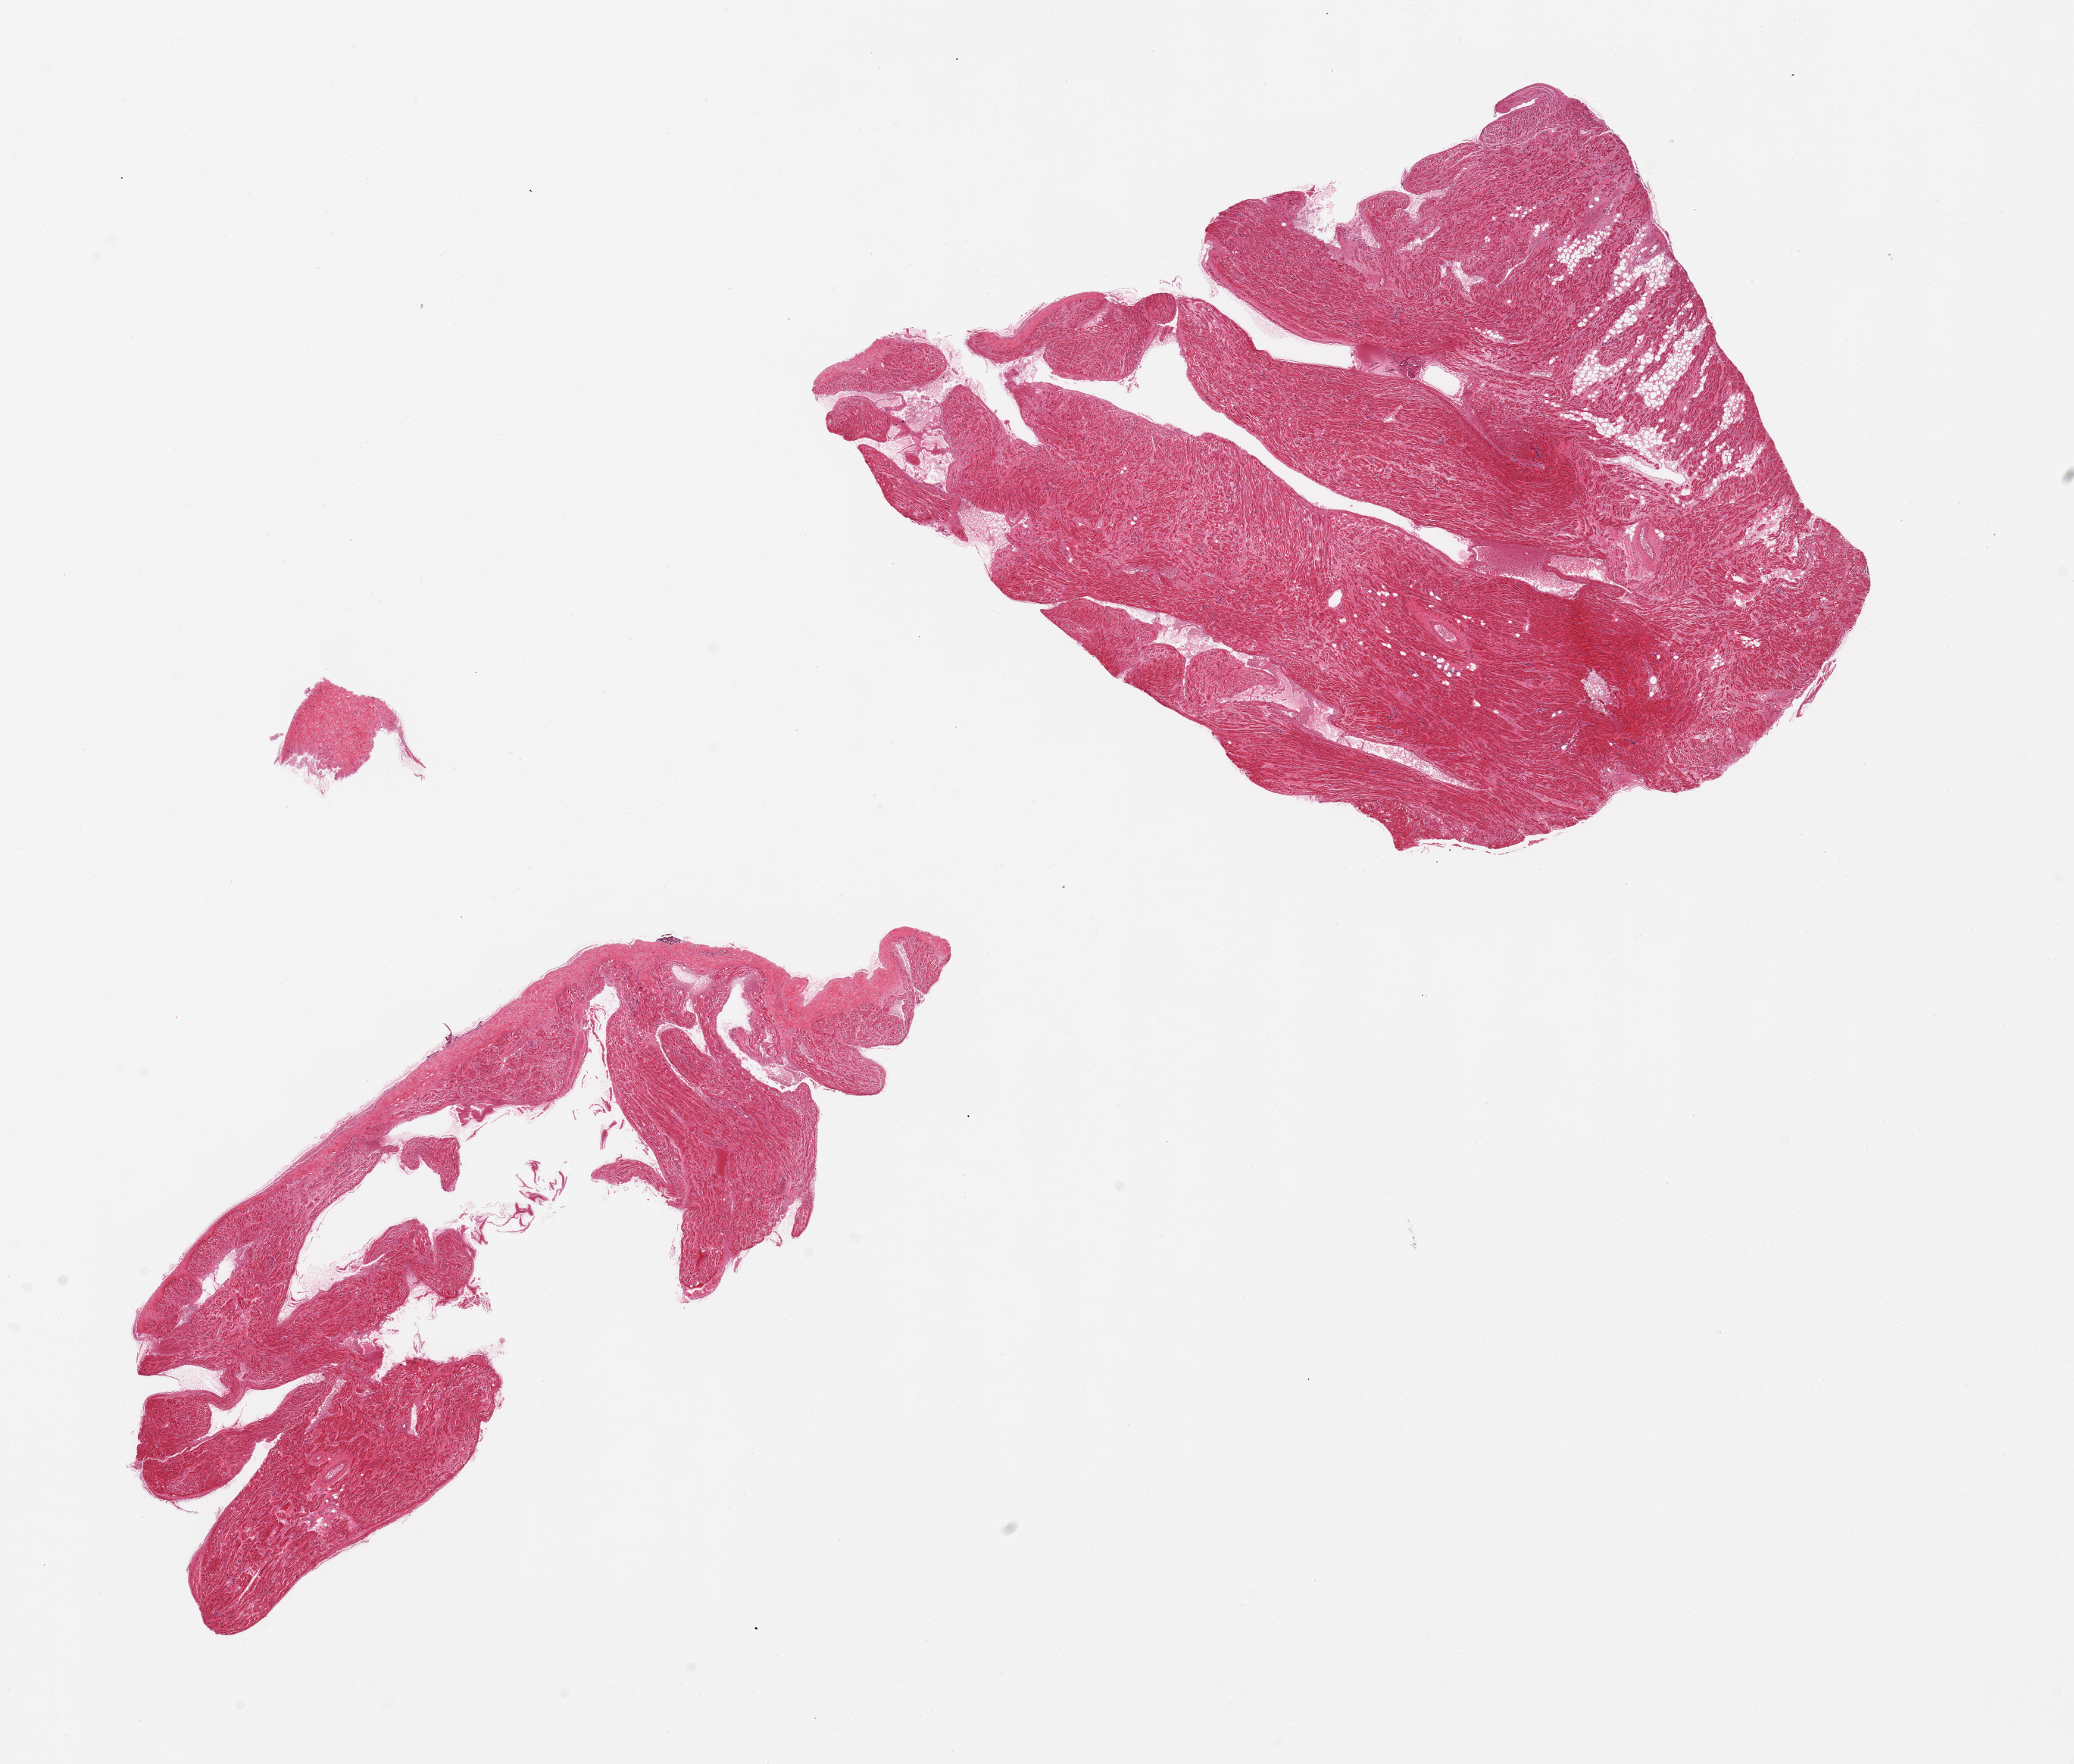
Whole-slide image, H&E stain, low-resolution overview of the scanned area, about 21.7 x 18.4 mm (slide scanned at 20x); PAXgene-fixed, paraffin-embedded tissue; section of auricular appendage (target tissue); donor tissue sample. Donor sex: male.
- review note (as recorded): 2 pieces